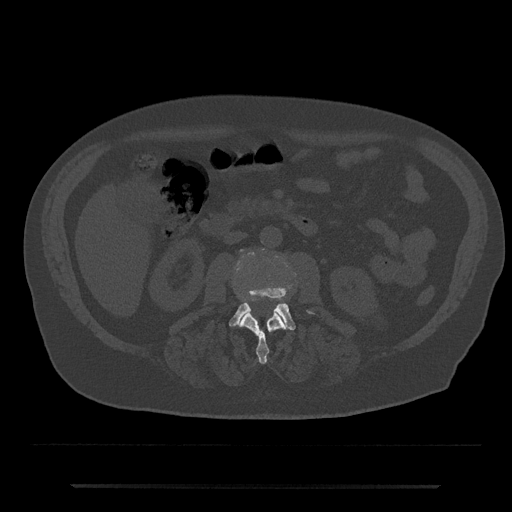
CT including the spine, one axial slice; slice 439 of 797 in the series (ordered by position); reconstruction kernel Br40s/3; 120 kVp; bone window (W 1800 / L 400 HU); 0.5 mm slice thickness; 512 × 512 image matrix. Male patient, age 80 years. From the clinical record (not read from this slice): primary cancer: prostate; vertebrae with lytic lesions (as recorded): L1, T11.
Outlined on this slice (semi-automatic segmentation, software-assisted and operator-edited):
- L2 vertebra: bounding box [x1, y1, x2, y2] px = [240, 310, 287, 364]
- L3 vertebra: [229, 249, 311, 330]